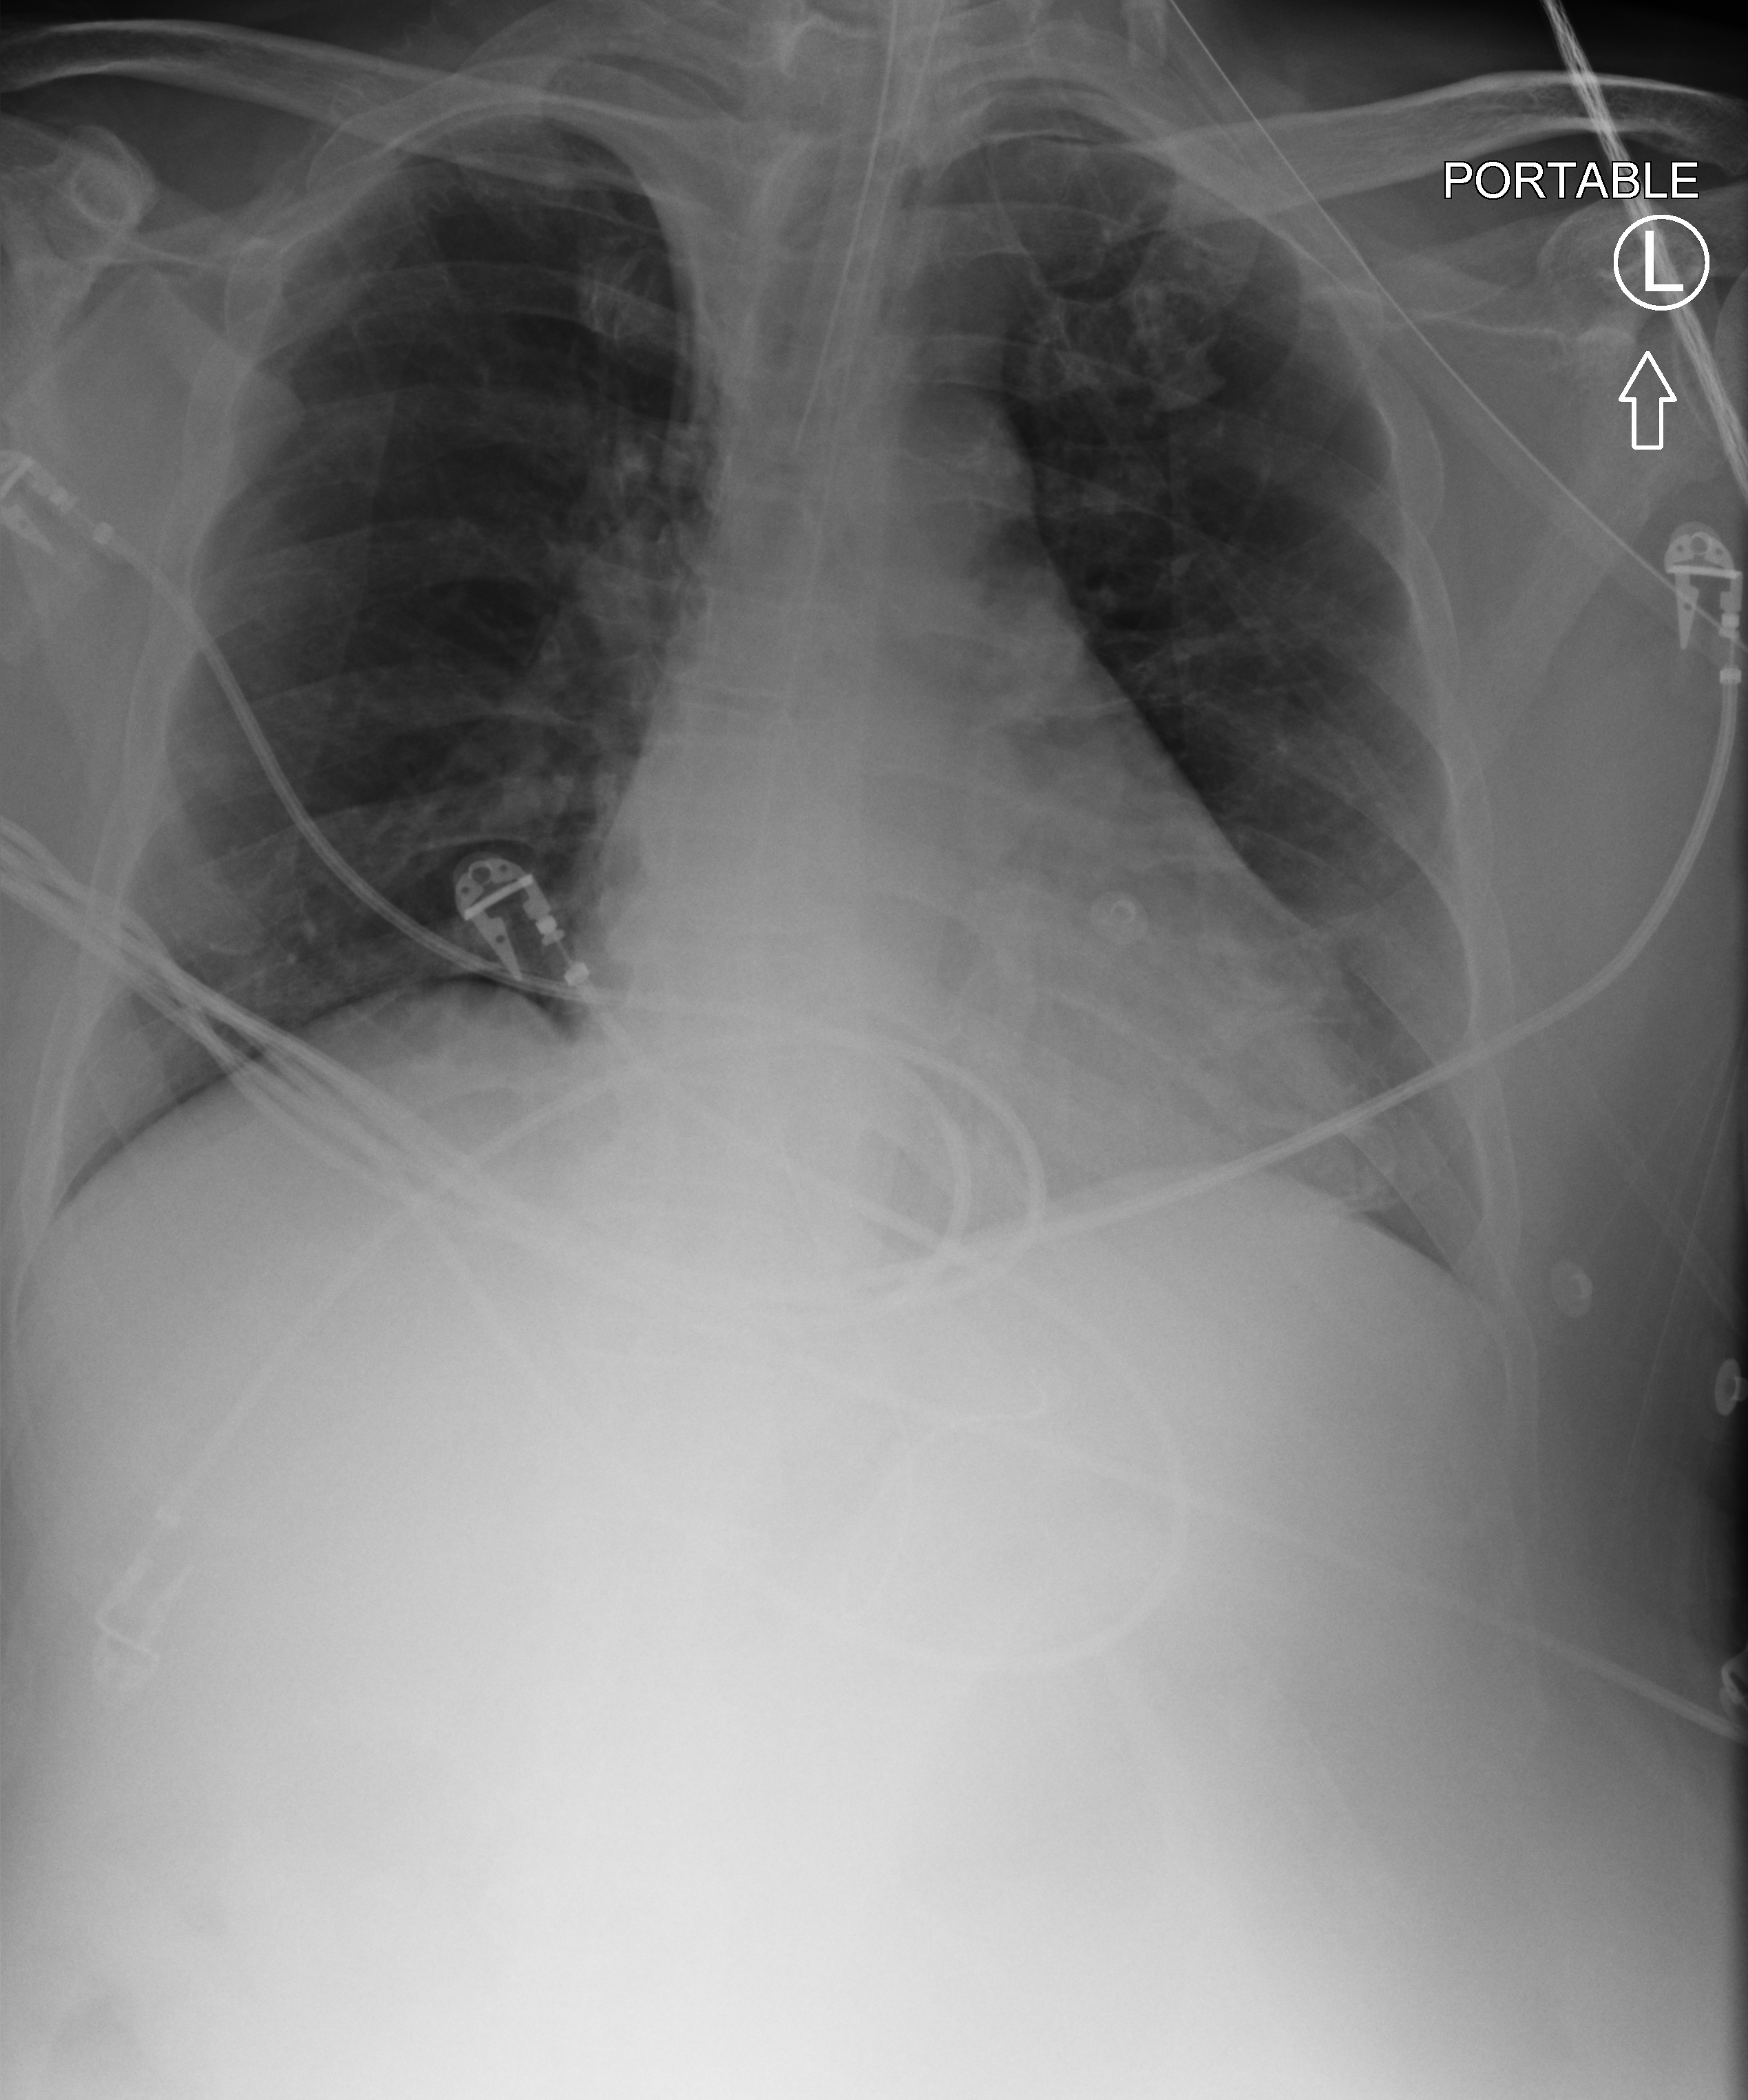
Chest X-ray (portable), anteroposterior (AP) projection. Patient hospitalised with COVID-19, aged 18–59 years.
From the hospital-stay record, not from the radiograph (when in the stay this image was taken is not recorded): mechanically ventilated during this hospital stay: yes.